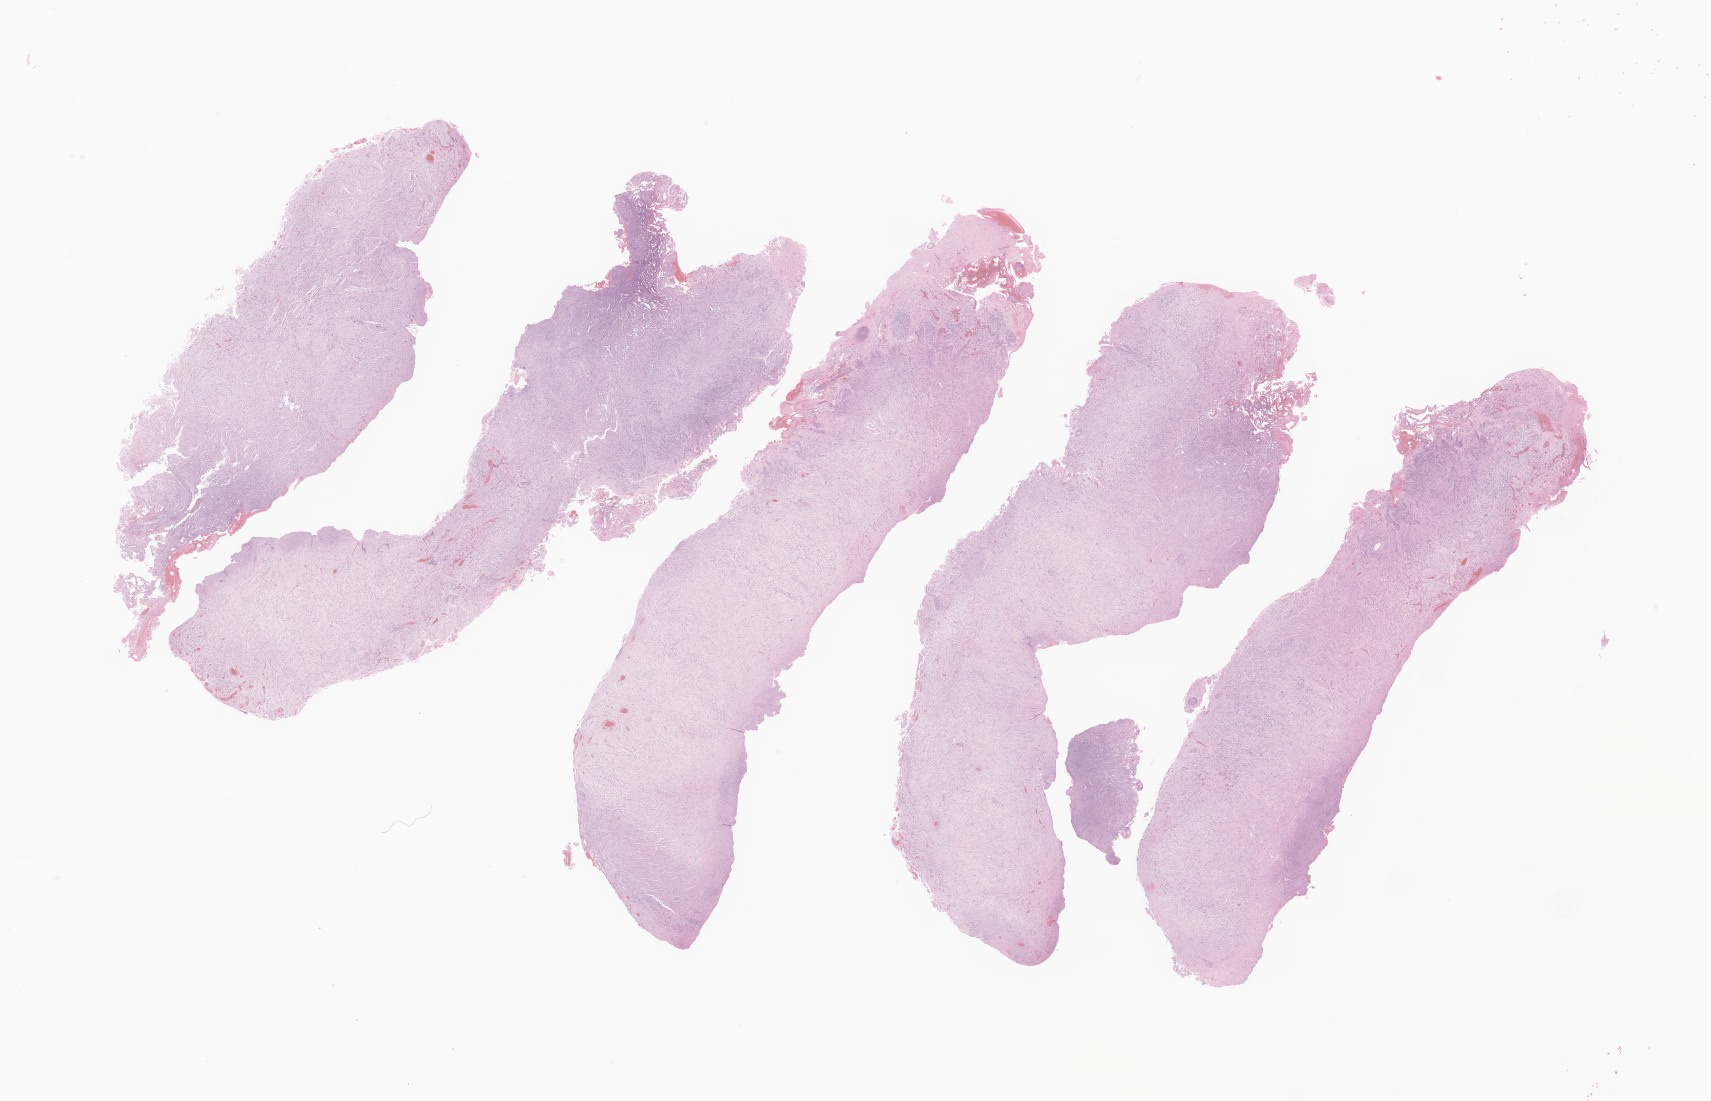
Whole-slide image, hematoxylin and eosin (H&E) stain of tumor tissue from the brain — shown as a low-resolution overview of the whole scanned area (about 28.9 x 18.6 mm); formalin-fixed, paraffin-embedded (FFPE) tissue. Patient: male, age 215 months (17 years 11 months).
Recorded diagnosis: Ganglioglioma, NOS.